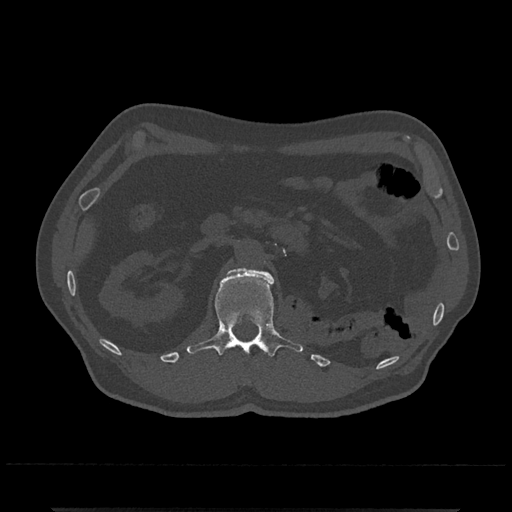
CT including the spine, one axial slice; slice 362 of 797 in the series (ordered by position); bone window (W 1800 / L 400 HU); 0.5 mm slice thickness; 512 × 512 image matrix, field of view 393 × 393 mm. Patient: male, 67 years. From the clinical record (not read from this slice): primary cancer: prostate.
Outlined on this slice (semi-automatically segmented with operator editing):
- L1 vertebra: box from (x=186, y=267) to (x=303, y=356) px